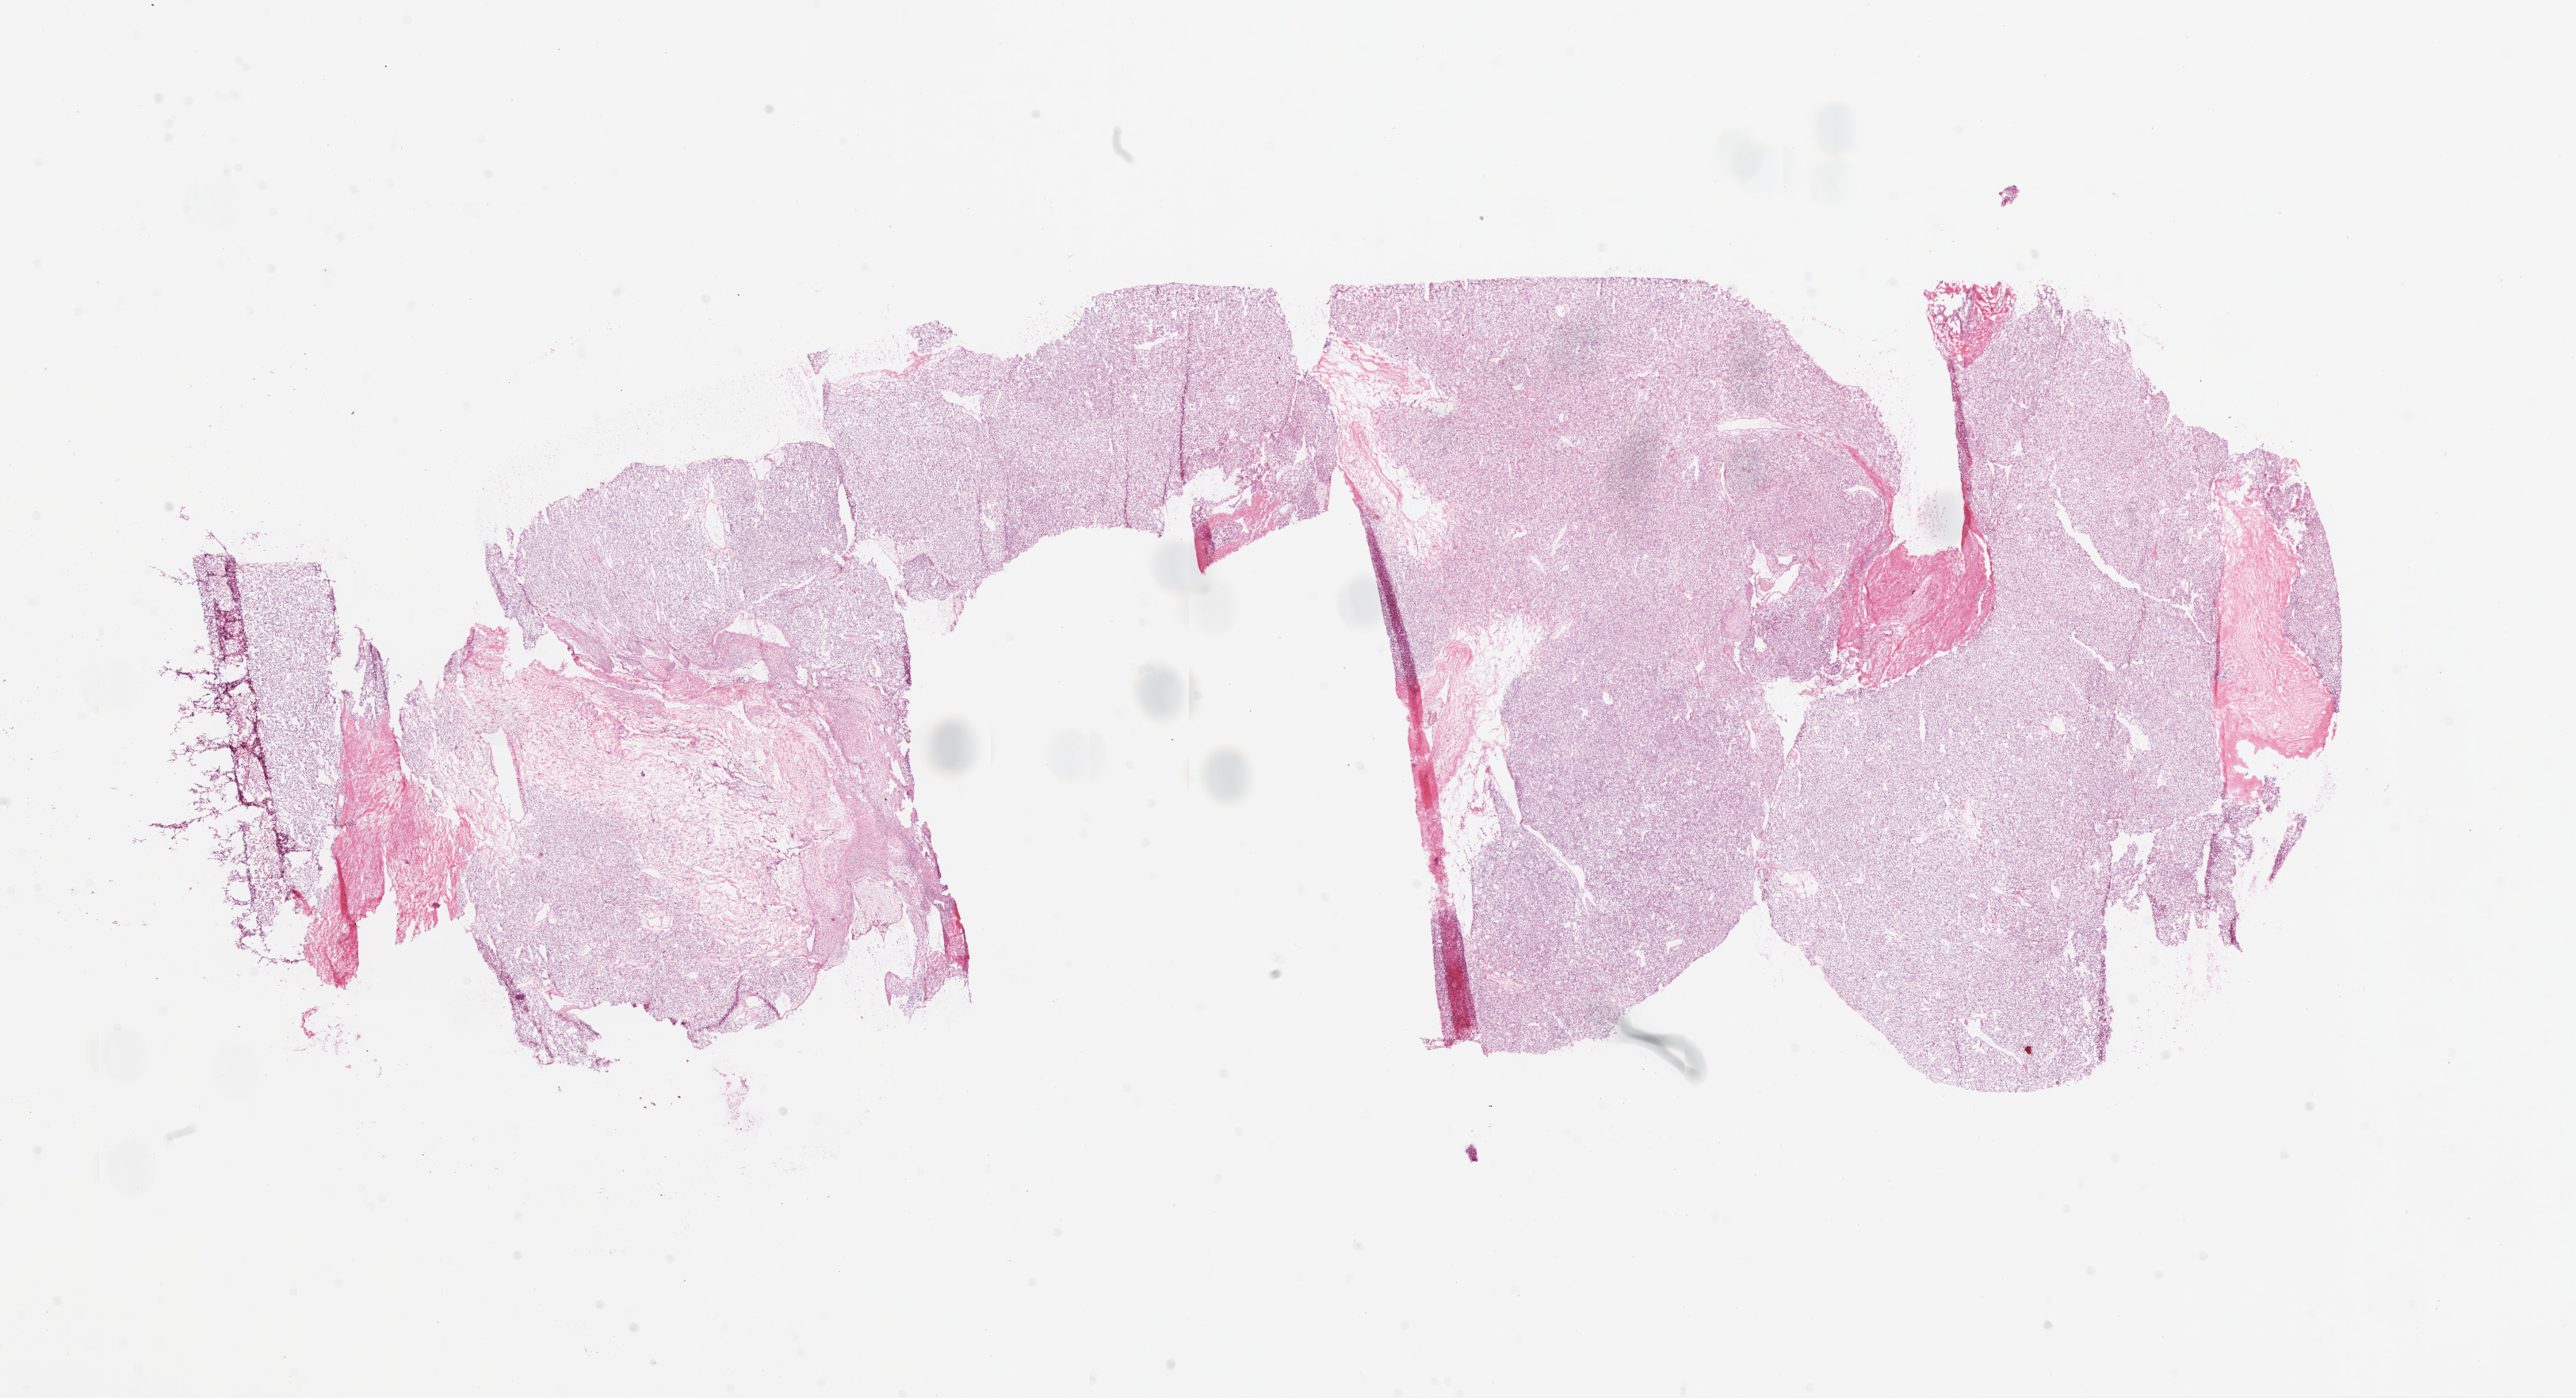
Whole-slide histology image, Hematoxylin and eosin (H&E) stained — low-resolution overview of the scanned area, about 26.1 x 14.2 mm. Frozen section. Sample: primary tumour, kidney. Female patient; age at initial diagnosis 67 years. Pathologist review of this section (percent, as recorded): tumour cells 95%, tumour nuclei 85%.
Diagnosis: Clear cell adenocarcinoma, NOS.